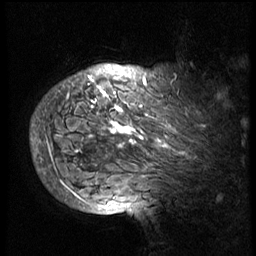
Breast MRI (dynamic contrast-enhanced), one sagittal slice. Position 60 of 74 along the scan axis. 3 images stored at this slice position (order not interpretable as contrast timing). 1.5 T. TE 4.2 ms, TR 8.9 ms. 256 × 256 image matrix, field of view 200 × 200 mm. Female patient, age 57 years. From the clinical record (not read from this slice): setting: breast cancer imaged before/during neoadjuvant chemotherapy; receptor status: HER2-positive.
Outlined on this slice (semi-automatically segmented with operator editing):
- analysis volume of interest (the breast-tissue region the enhancement analysis was run in; not a lesion): bounding box <40,62,237,175> (left, top, right, bottom; pixels)
- tumour enhancement mask (voxels above the 140 % enhancement threshold inside the analysis volume of interest): <40,76,206,175>